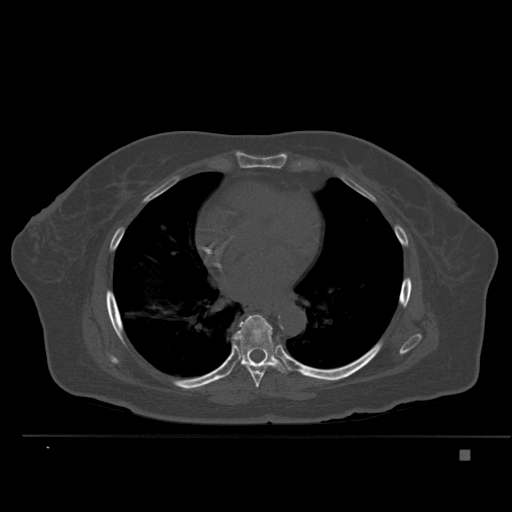
CT including the spine, one axial slice. Position 317 of 477 along the scan axis. Bone window (W 1800 / L 400 HU). 1.5 mm slice thickness. 512 × 512 image matrix, field of view 422 × 422 mm. Patient: female, 74 years. Case-level facts recorded for this patient, not image findings: primary cancer: colon.
Structures marked on this image (semi-automatically segmented with operator editing):
- T7 vertebra: bounding box (x1, y1, x2, y2) in pixels: (241, 364, 266, 388)
- T8 vertebra: (233, 314, 289, 374)